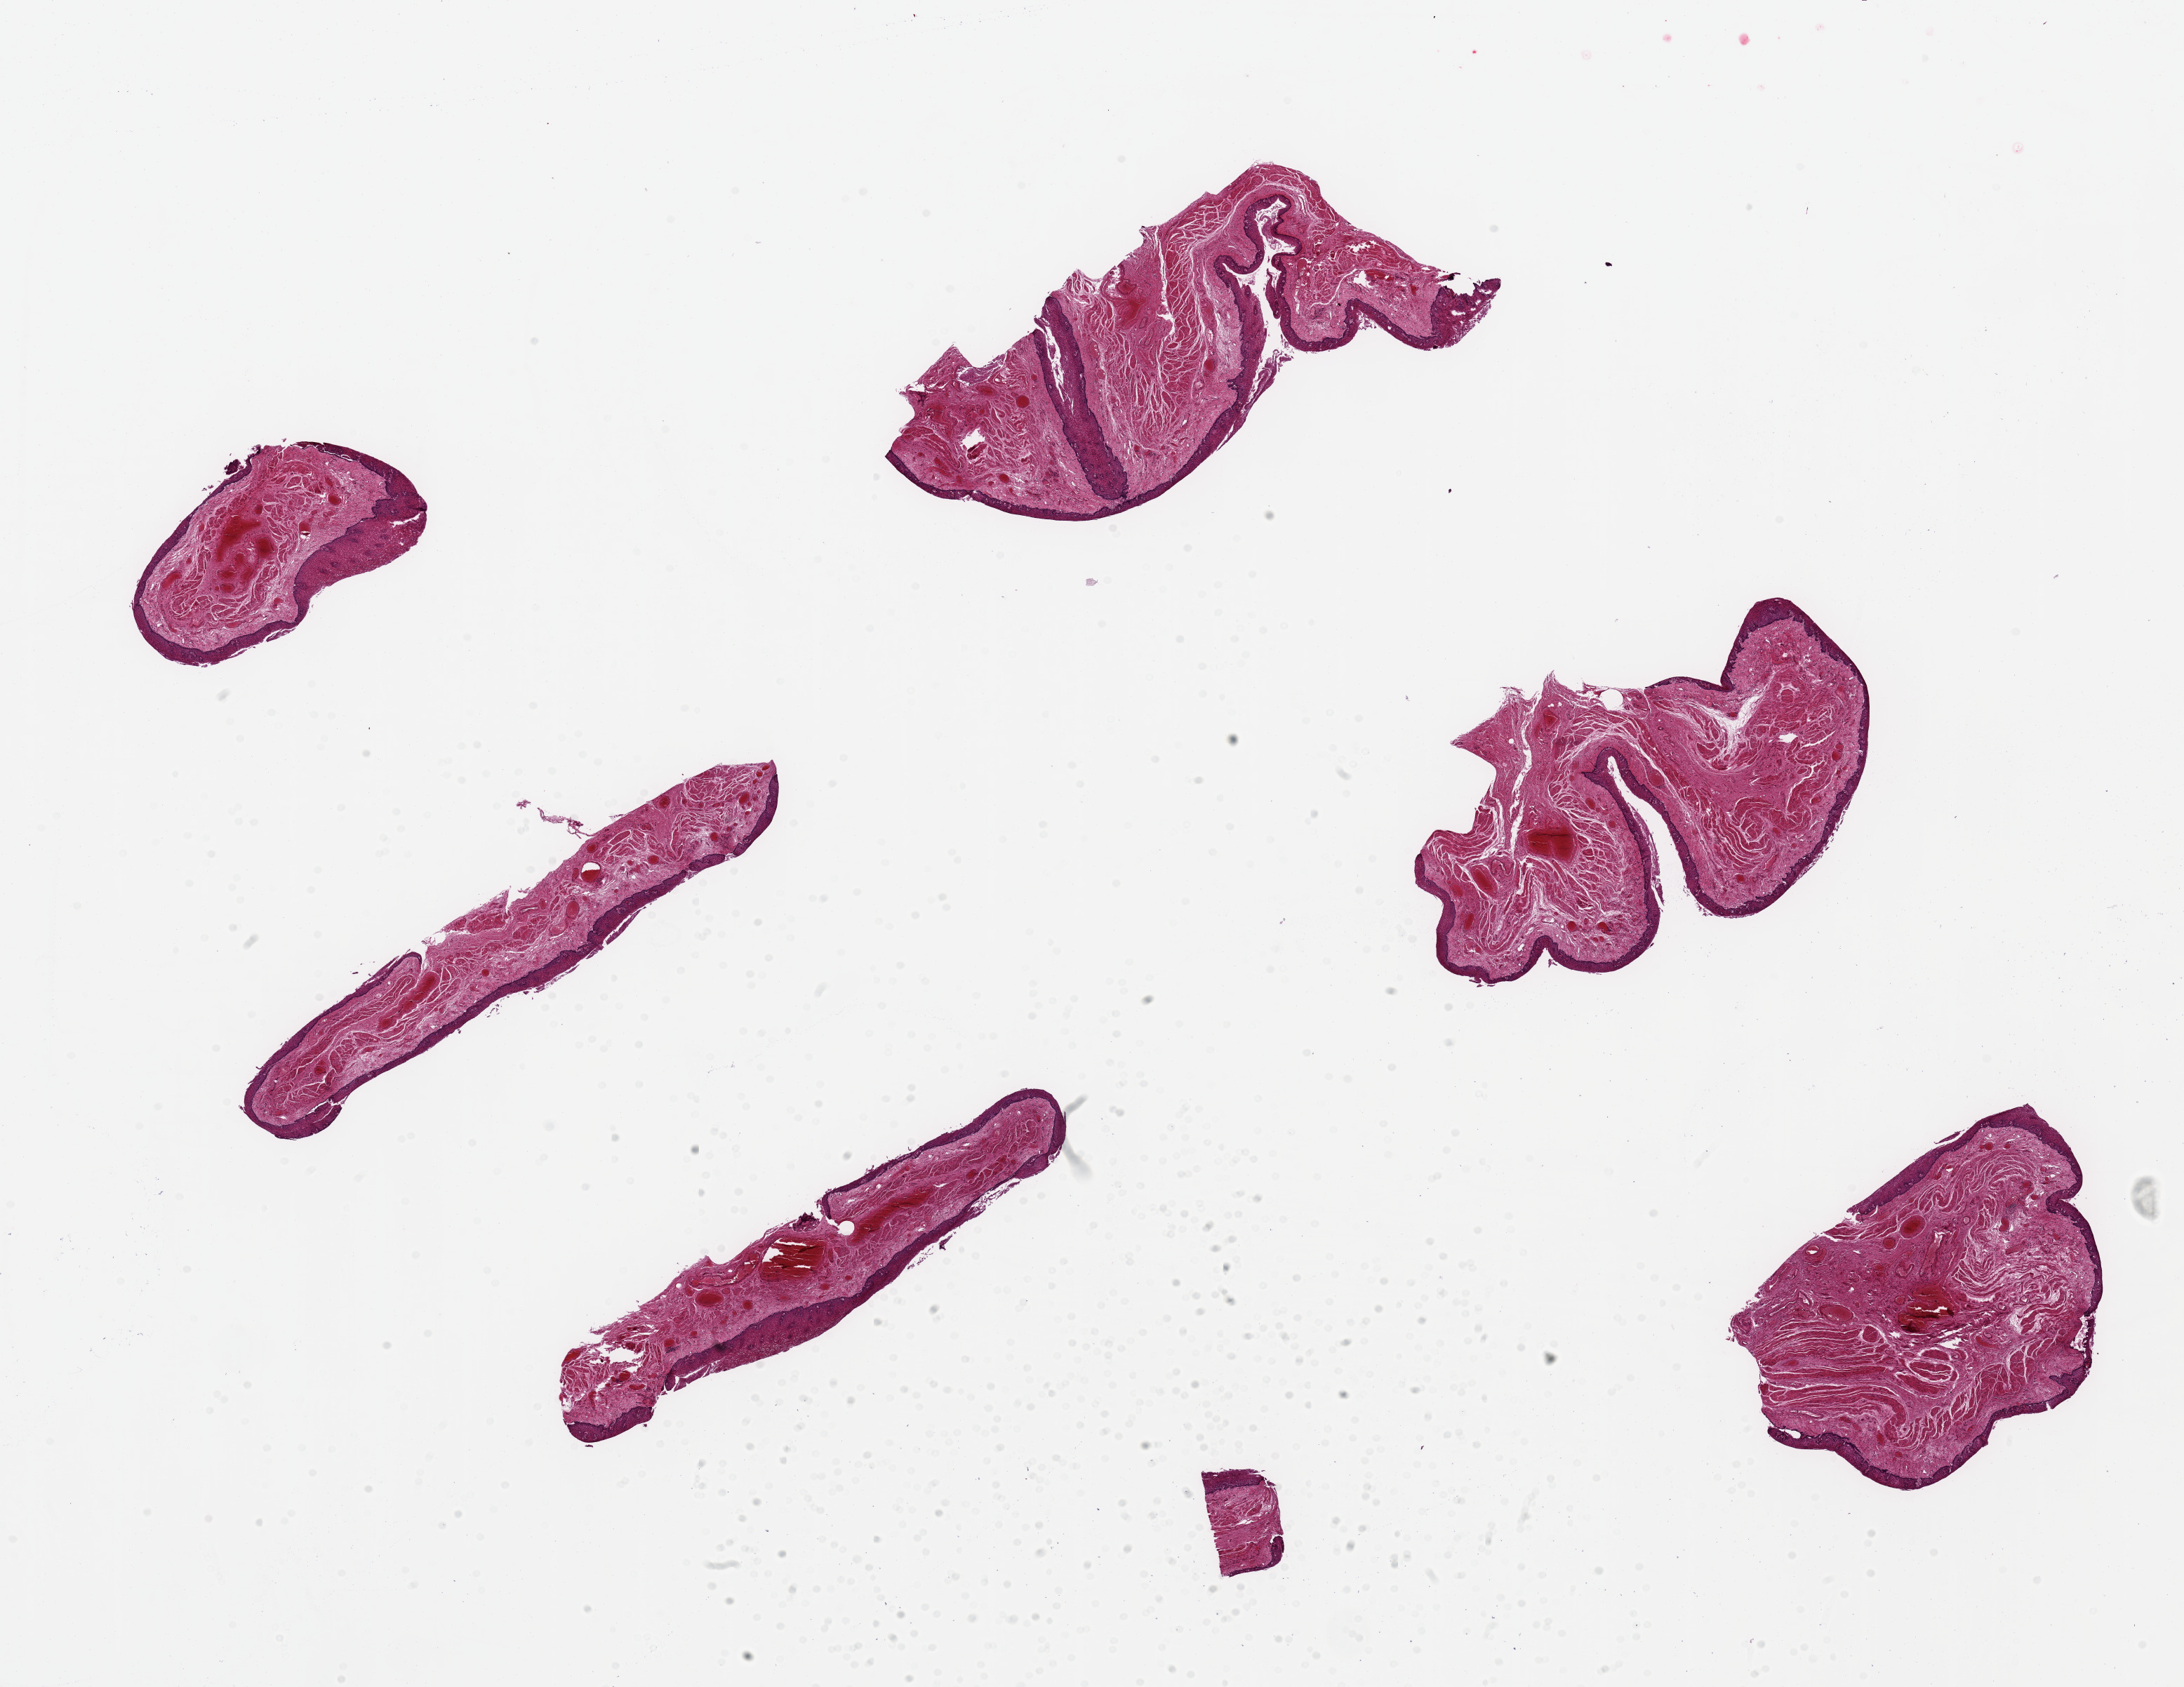
Whole-slide image, hematoxylin and eosin (H&E) stain — a low-resolution overview of the entire scanned area, about 24.6 x 19.0 mm (slide scanned at 20x); PAXgene-fixed paraffin-embedded (PFPE) section; target tissue: esophageal mucous membrane; donor tissue sample. Male donor.
Pathologist's review note for this sample: 6 ~ 7x3mm pieces. Squamous mucosa is ~10% of thickness.